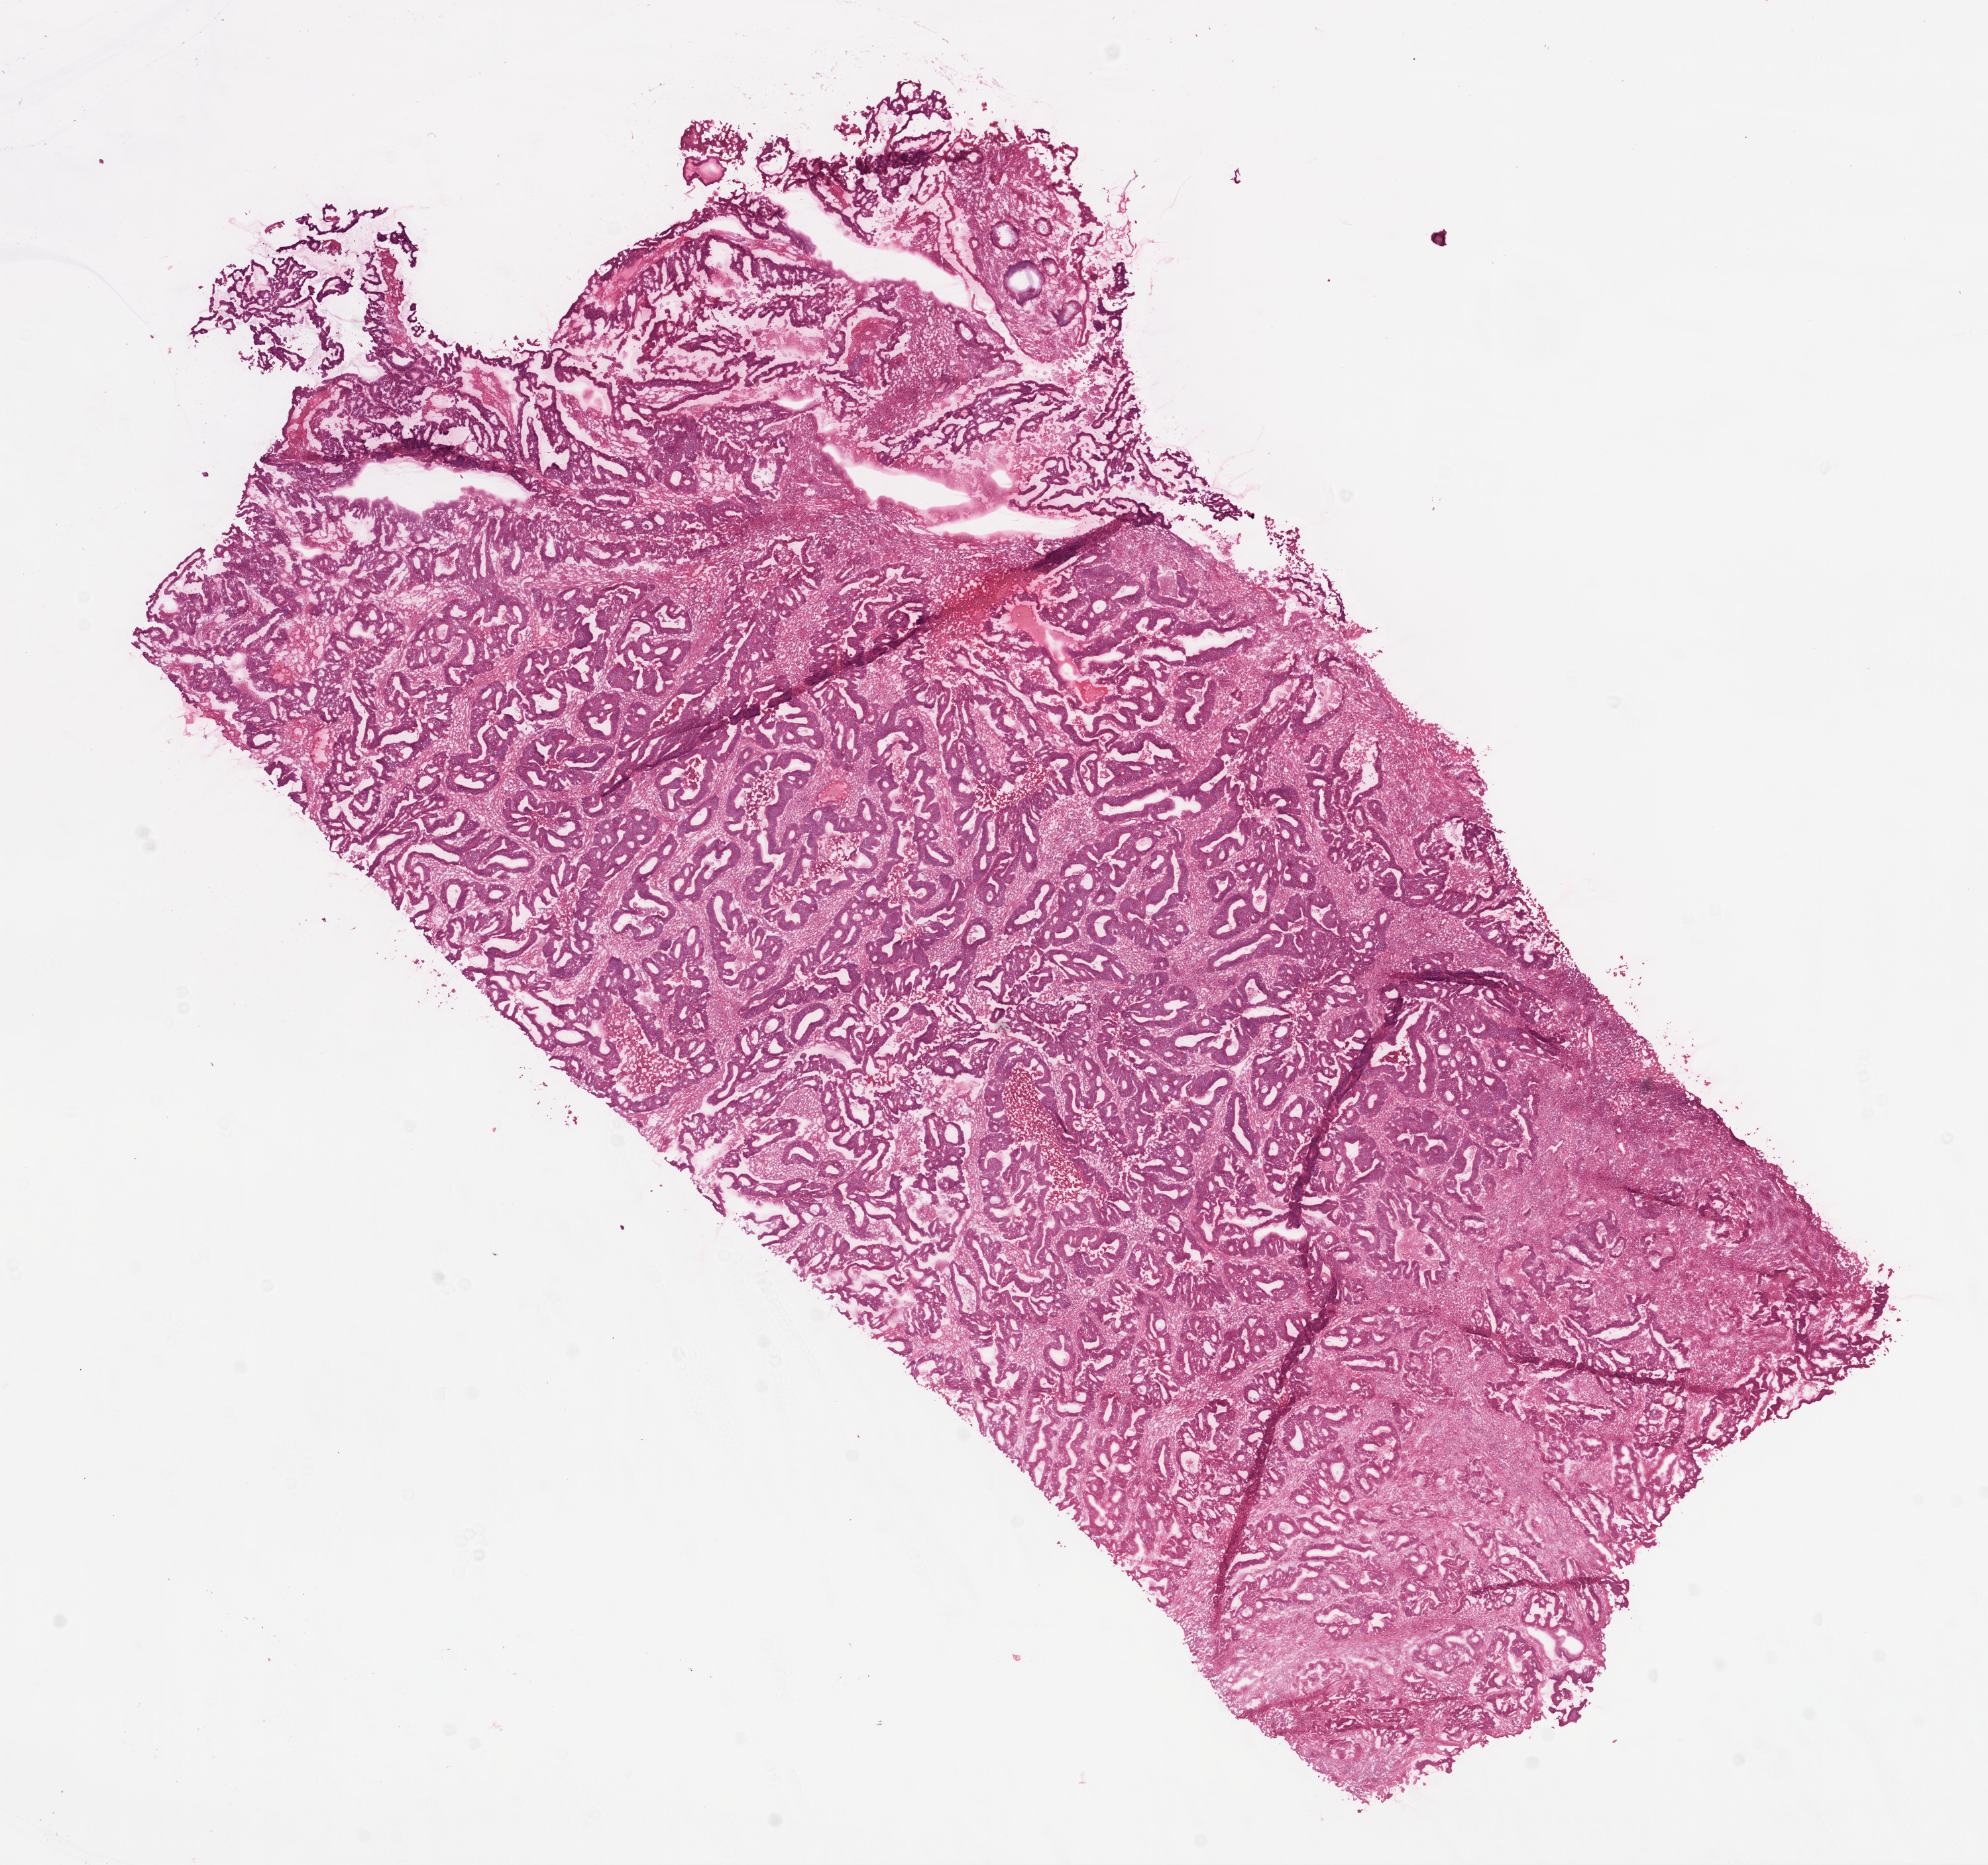
Whole-slide histology image, H&E-stained — low-resolution overview of the scanned area, about 12.0 x 11.3 mm (slide scanned at 20x). Frozen section from the top of the tissue portion. Colon, primary tumour sample. Male, age 61 years at initial diagnosis. Slide review estimates, as recorded: tumour cells 80%, tumour nuclei 75%, normal cells 0%, stromal cells 15%, necrosis 5%.
• AJCC pathologic stage: IIA
• diagnosis: Adenocarcinoma, NOS (cecum)